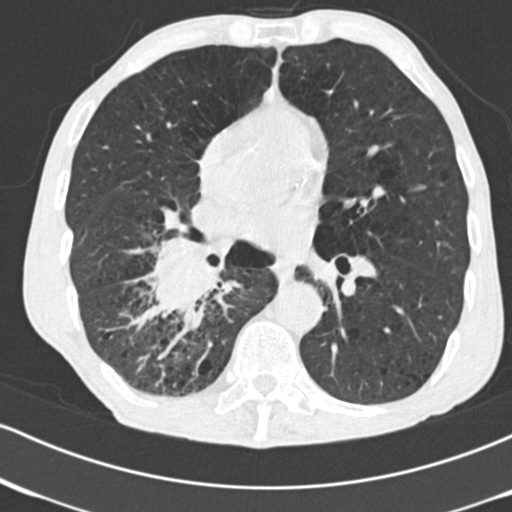
Axial slice from a low-dose chest CT screening exam; second annual screen; lung window (W 1500 / L -600 HU); 2 mm slice thickness; standard (soft-tissue) reconstruction kernel (B30f); 512 × 512 image matrix, field of view 316 × 316 mm. Male, age 64 years at enrolment. Current smoker at enrolment.
• Expert reader's lesion annotation, box from (x=126, y=226) to (x=242, y=335) px.
• Screening reader's record for this exam (one nodule recorded; not confirmed to be the boxed lesion): non-calcified nodule or mass ≥4 mm, 52 × 37 mm, spiculated (stellate) margins, soft tissue attenuation, pre-existing on the prior screen: no.
• Participant outcome: lung cancer diagnosed 28 days after this screen — adenocarcinoma, NOS, right lower lobe, stage IV (AJCC 6th edition), 60 mm at pathology.